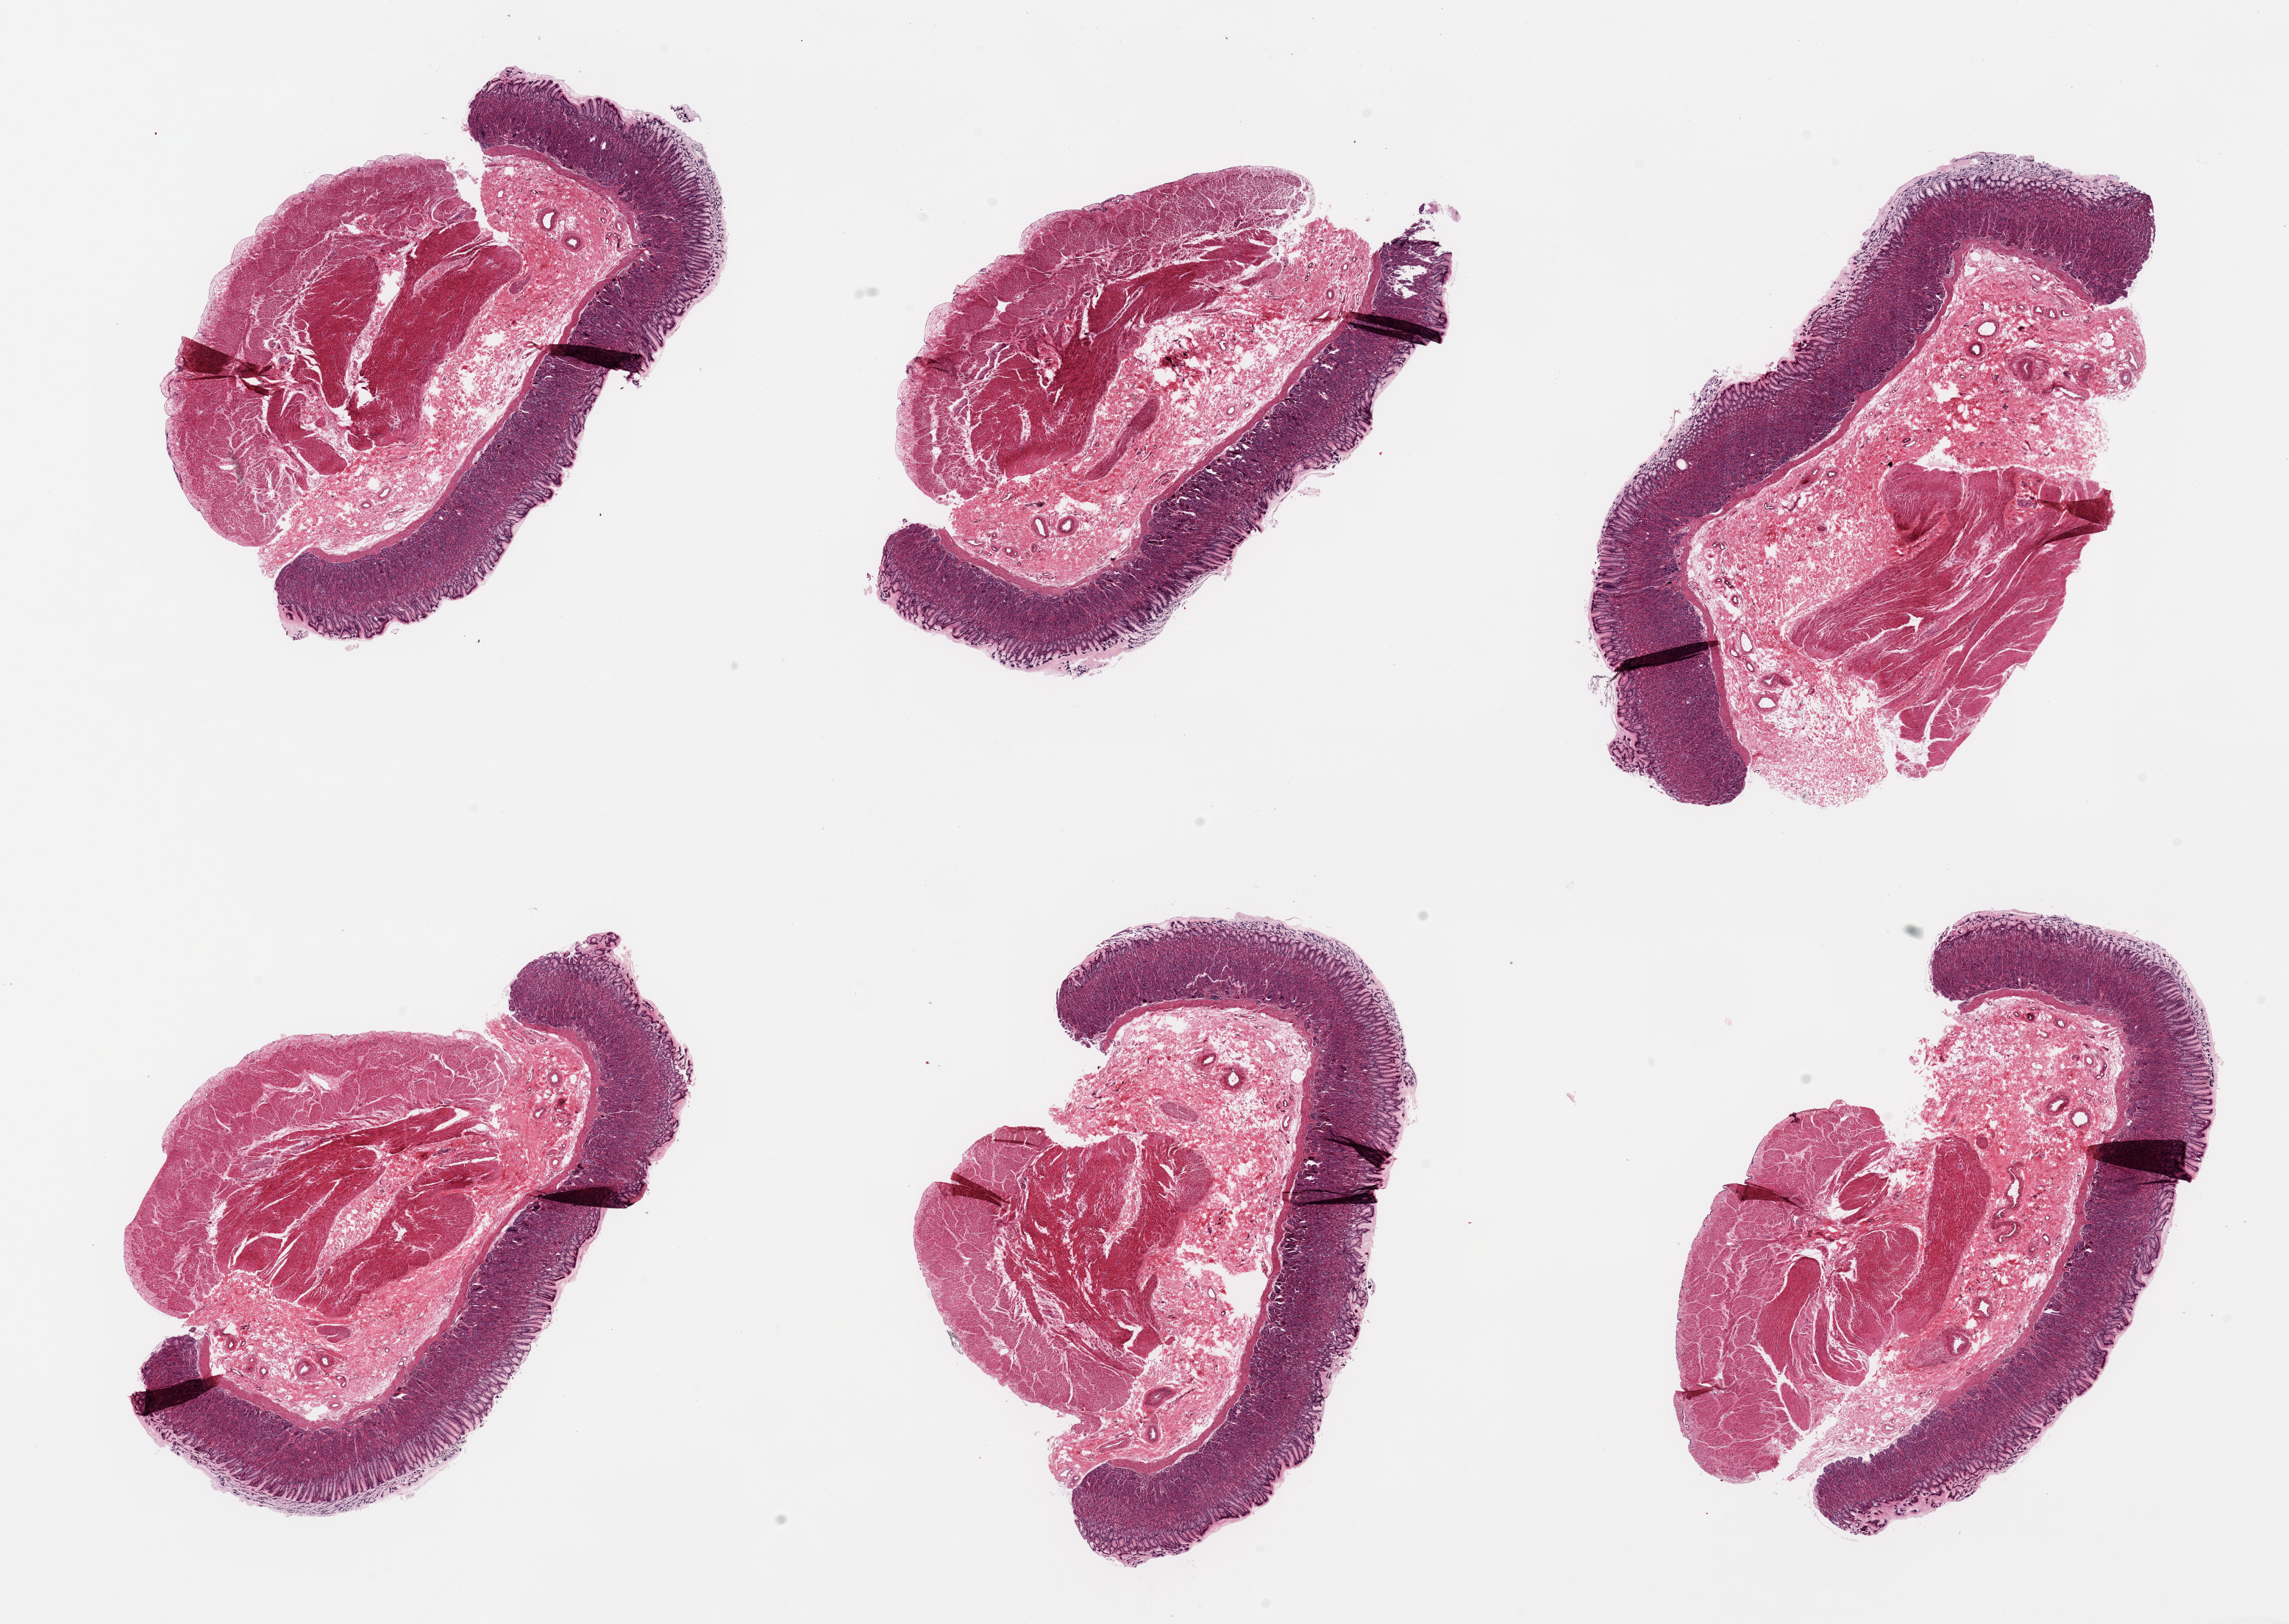
Hematoxylin and eosin (H&E) whole-slide image, shown as a low-resolution overview of the whole scanned area (about 24.6 x 17.5 mm, acquisition: 20x scan); PAXgene-fixed, paraffin-embedded tissue; section of stomach (target tissue); tissue donor sample.
* review note (as recorded): 6 pieces; well preserved mucosa; full thickness specimens